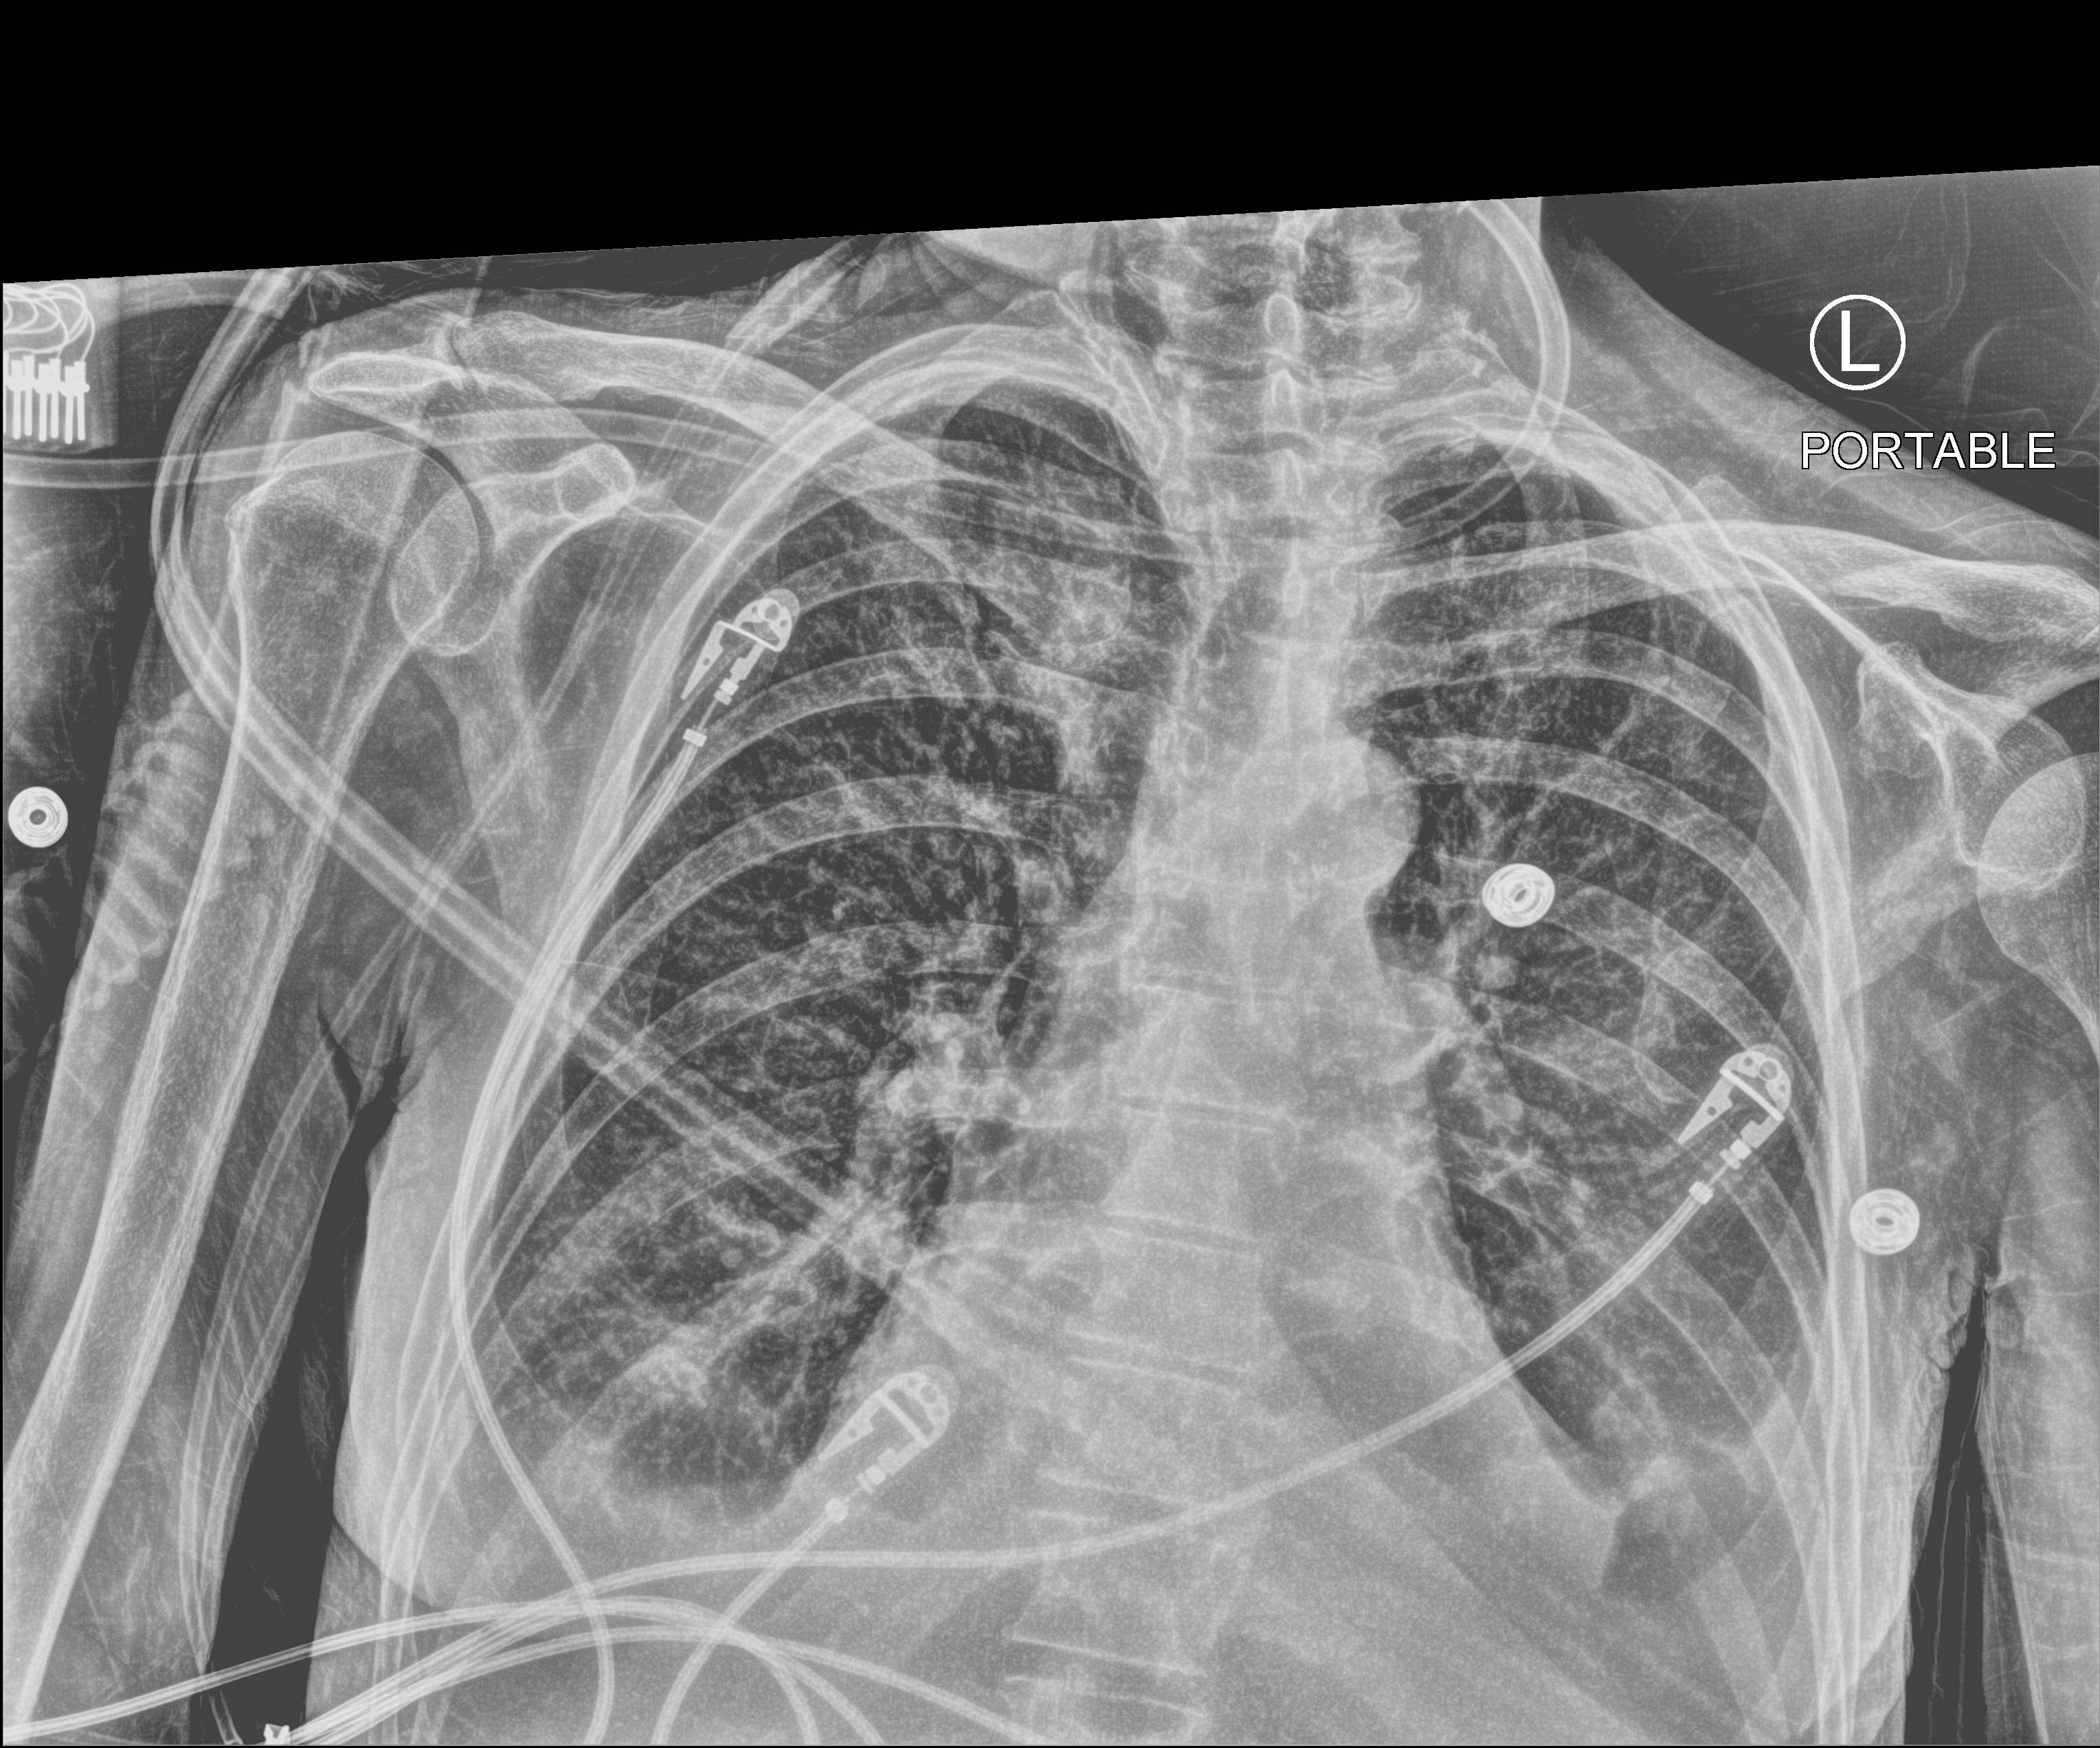
Portable chest radiograph, anteroposterior (AP) projection. Patient hospitalised with COVID-19; female, aged 60–74 years.
Admission-level facts for this patient (not findings on this image; timing relative to this image not recorded): admitted to intensive care during this hospital stay: yes; length of hospital stay: 38 days.